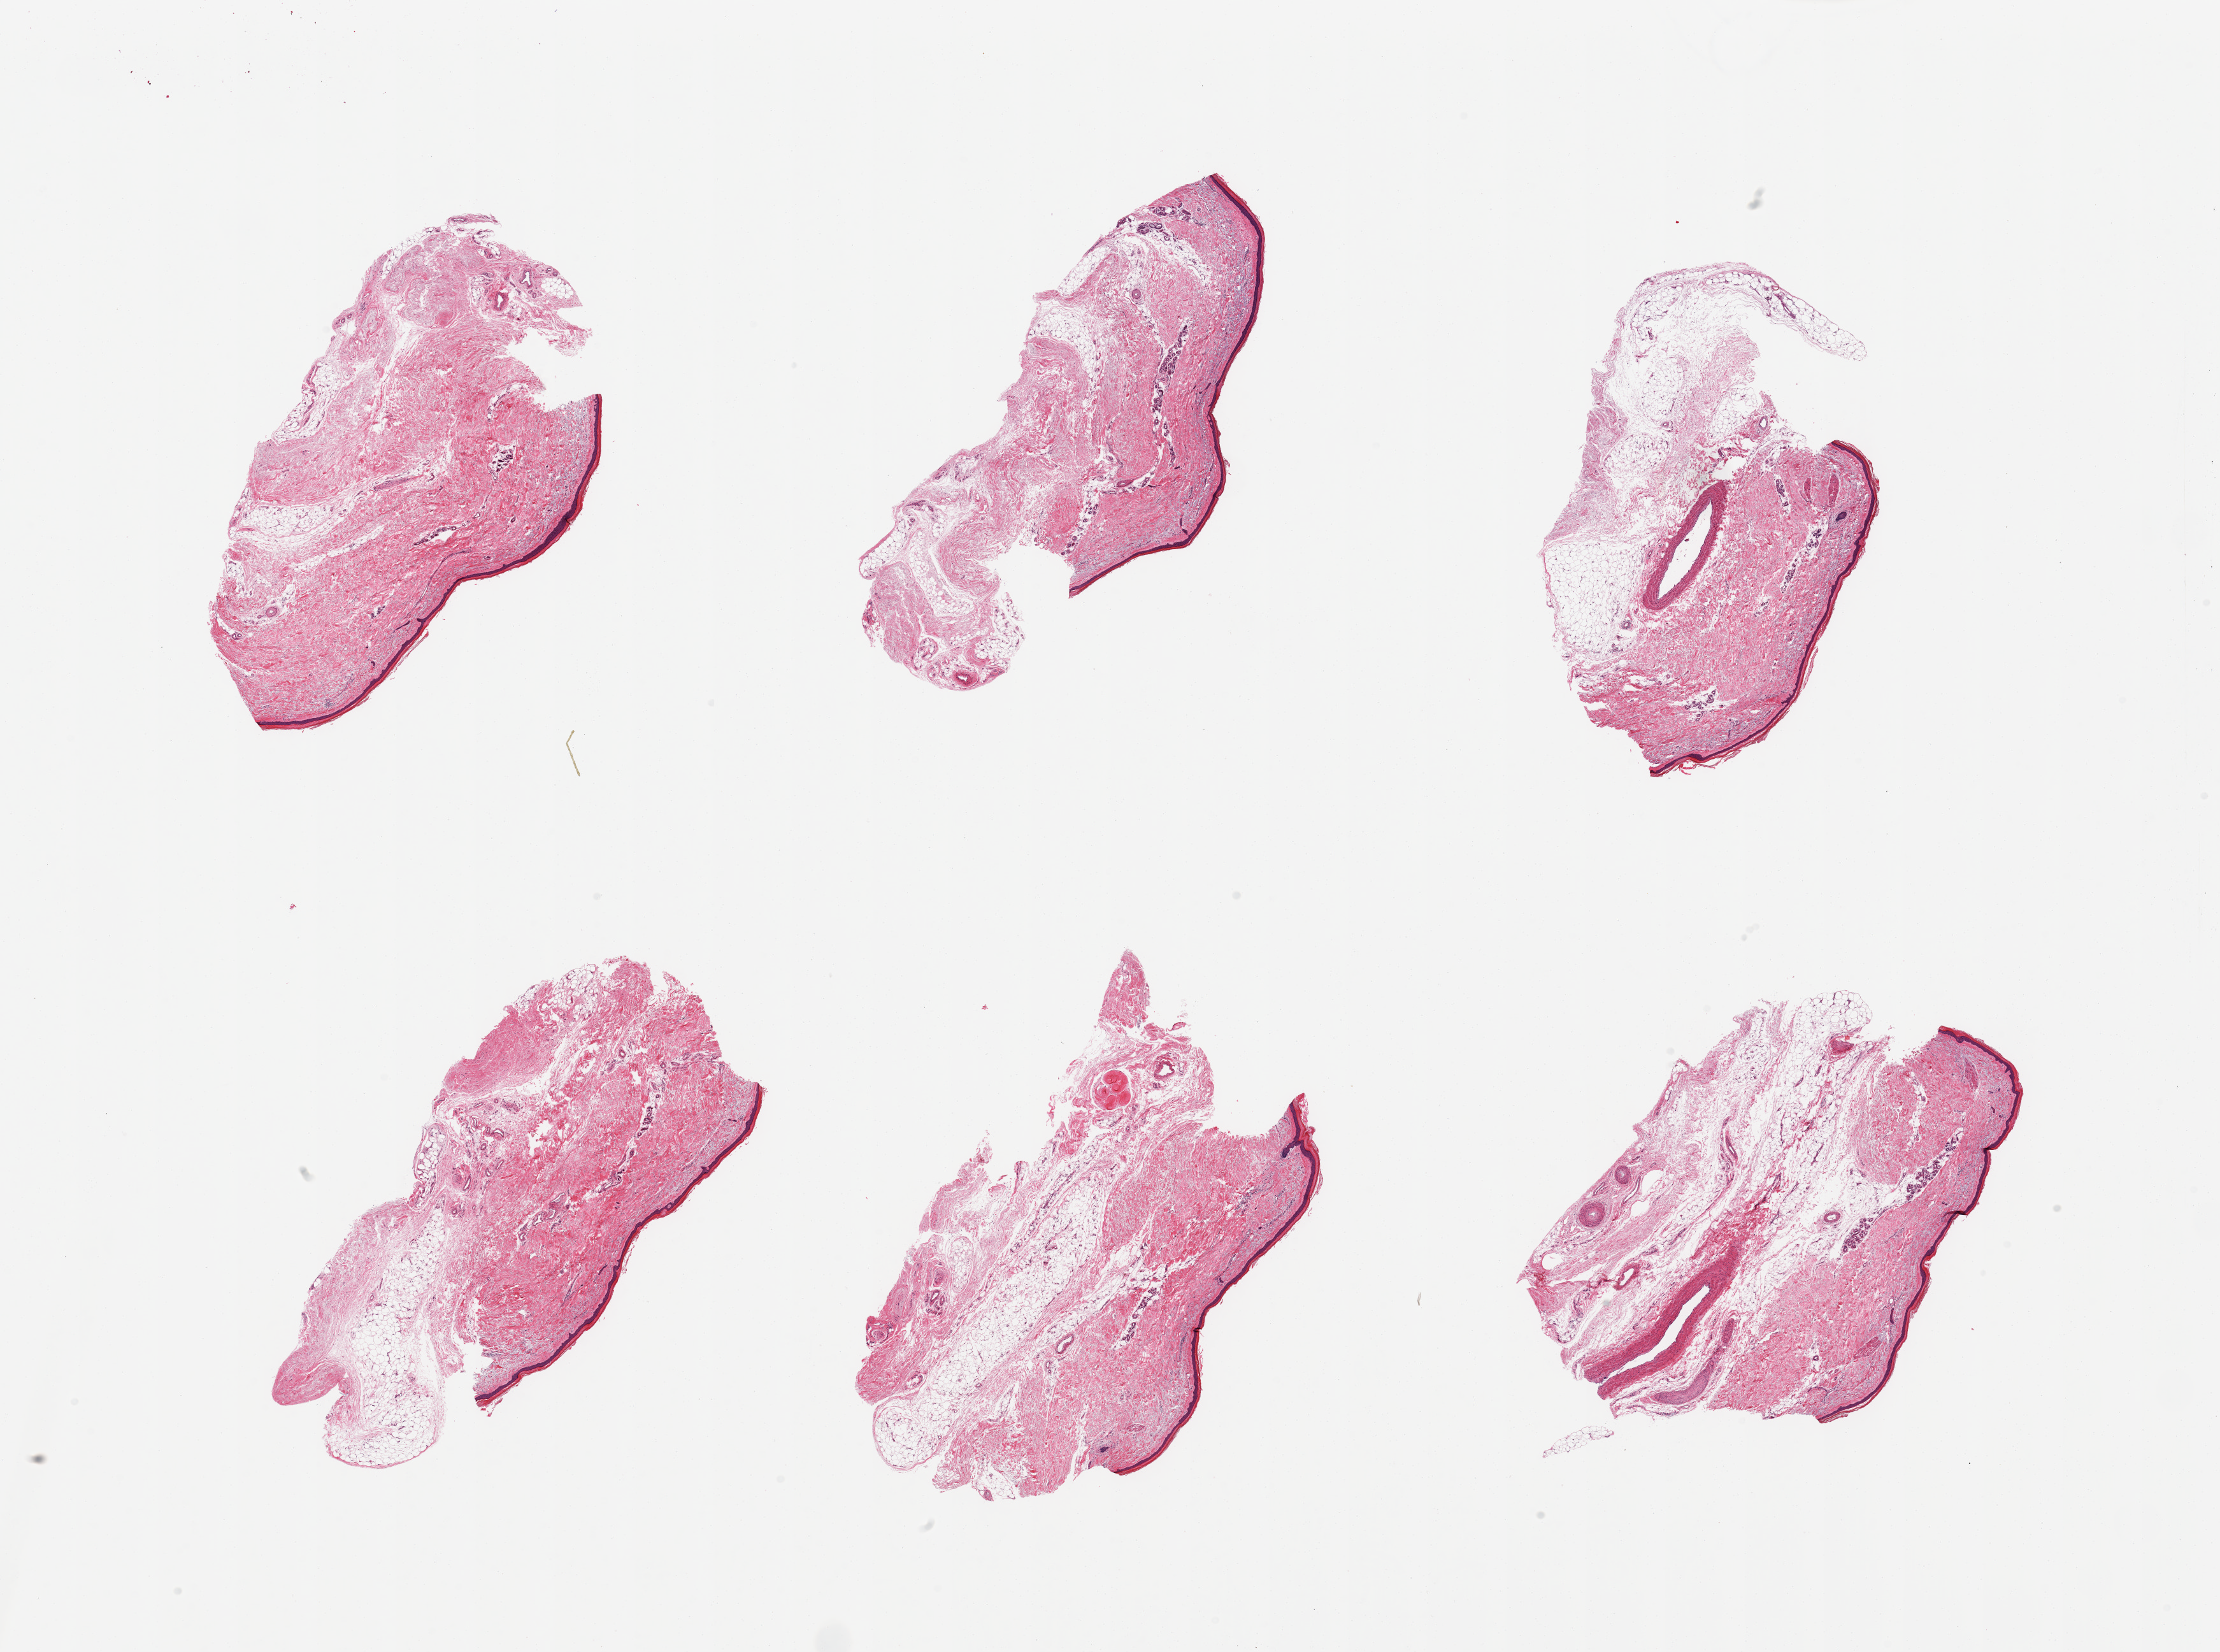
Digitized hematoxylin and eosin (H&E)-stained section, brightfield — shown as a low-resolution overview of the whole scanned area (about 27.6 x 20.5 mm), PAXgene-fixed, paraffin-embedded tissue, section of skin of lower leg (target tissue), tissue donor sample. Donor sex: female.
- review note (as recorded): 6 pieces; half are poorly trimmed with fat and several large arteries